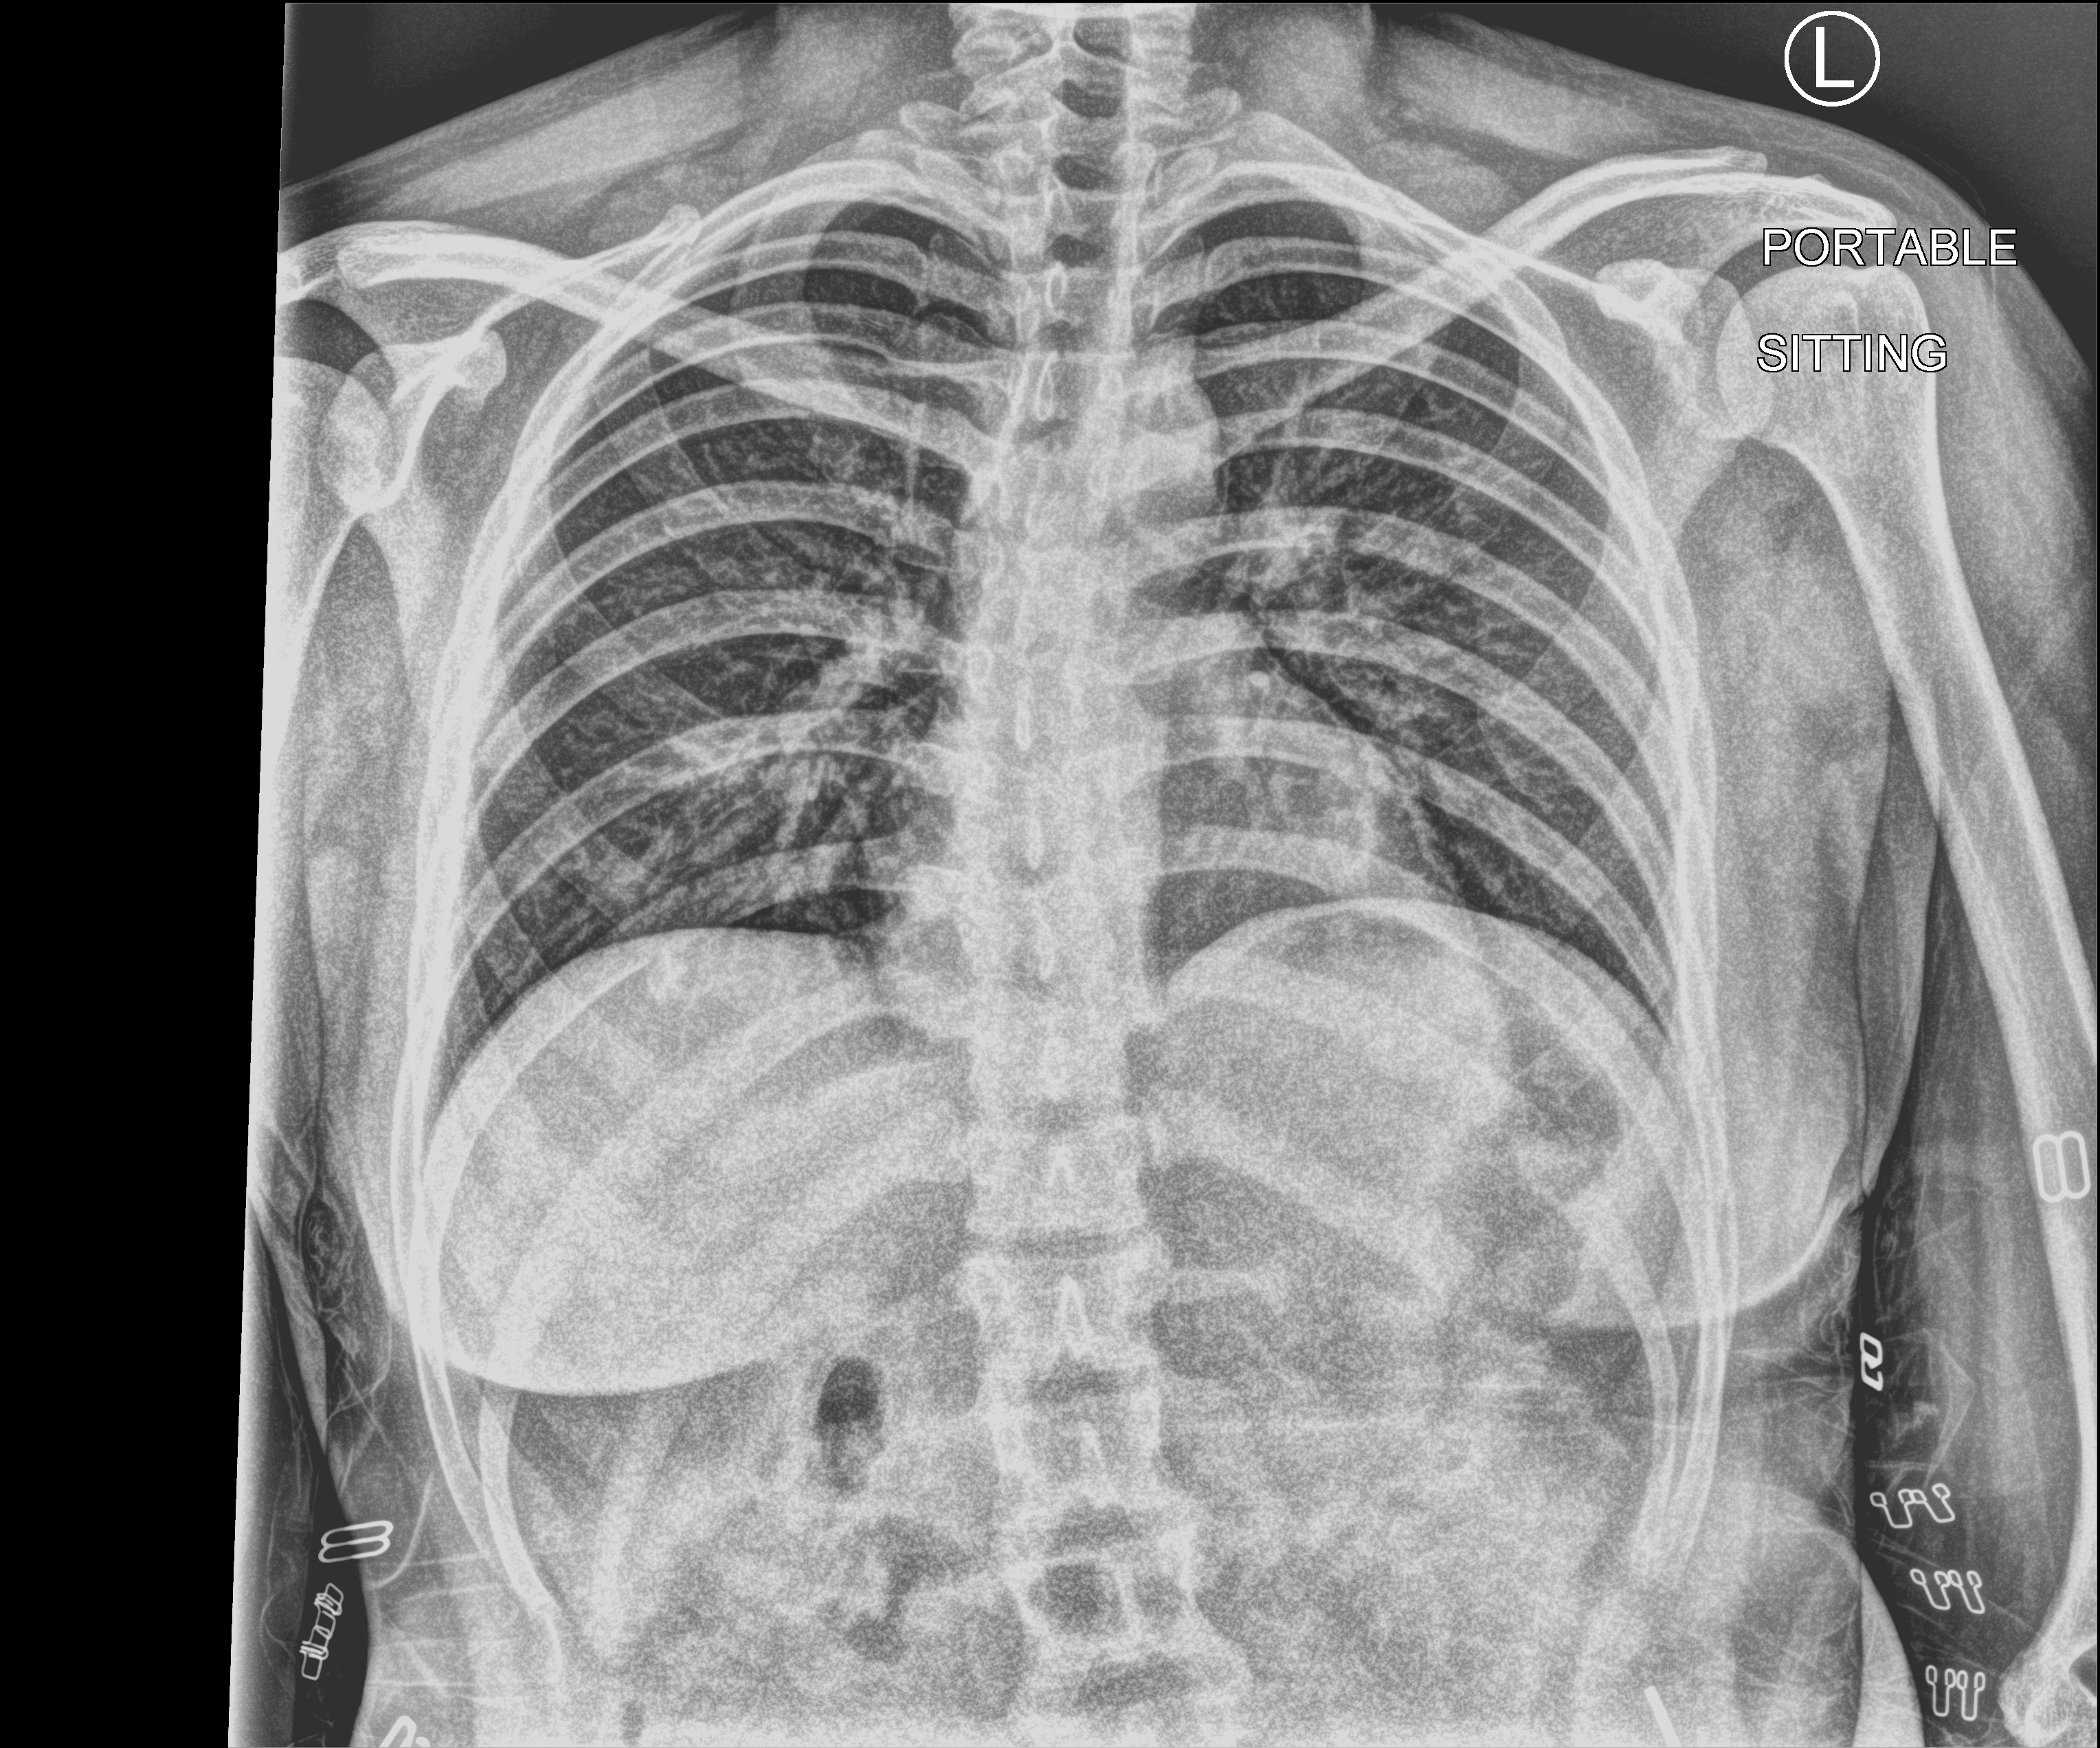
Chest X-ray (portable). Patient hospitalised with COVID-19; female, aged 18–59 years.
From the hospital-stay record, not from the radiograph (when in the stay this image was taken is not recorded):
- diabetes (admission record): no